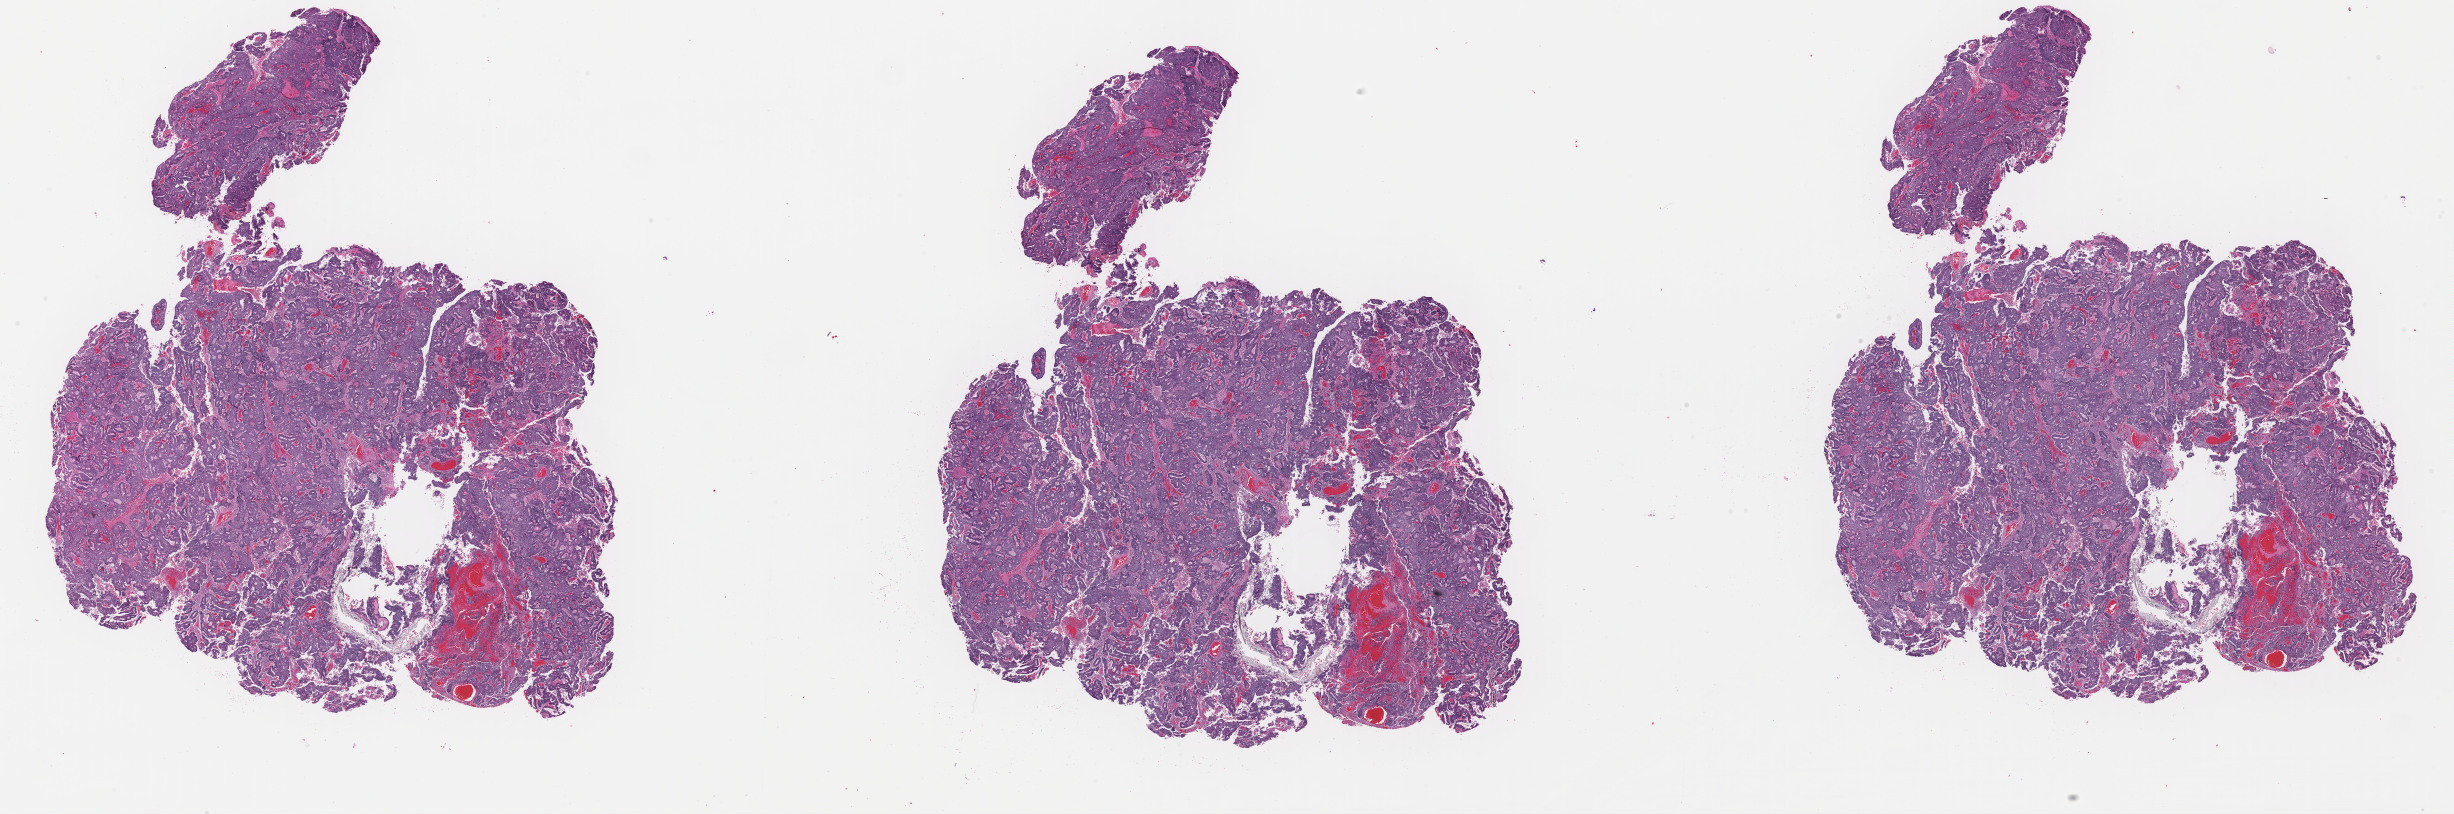
Whole-slide histology image, H&E — low-resolution overview of the scanned area, about 38.8 x 12.9 mm; FFPE section; uterus, primary tumour sample. Female patient; age at initial diagnosis 66 years.
Histologic diagnosis: Endometrioid adenocarcinoma, NOS (endometrium).